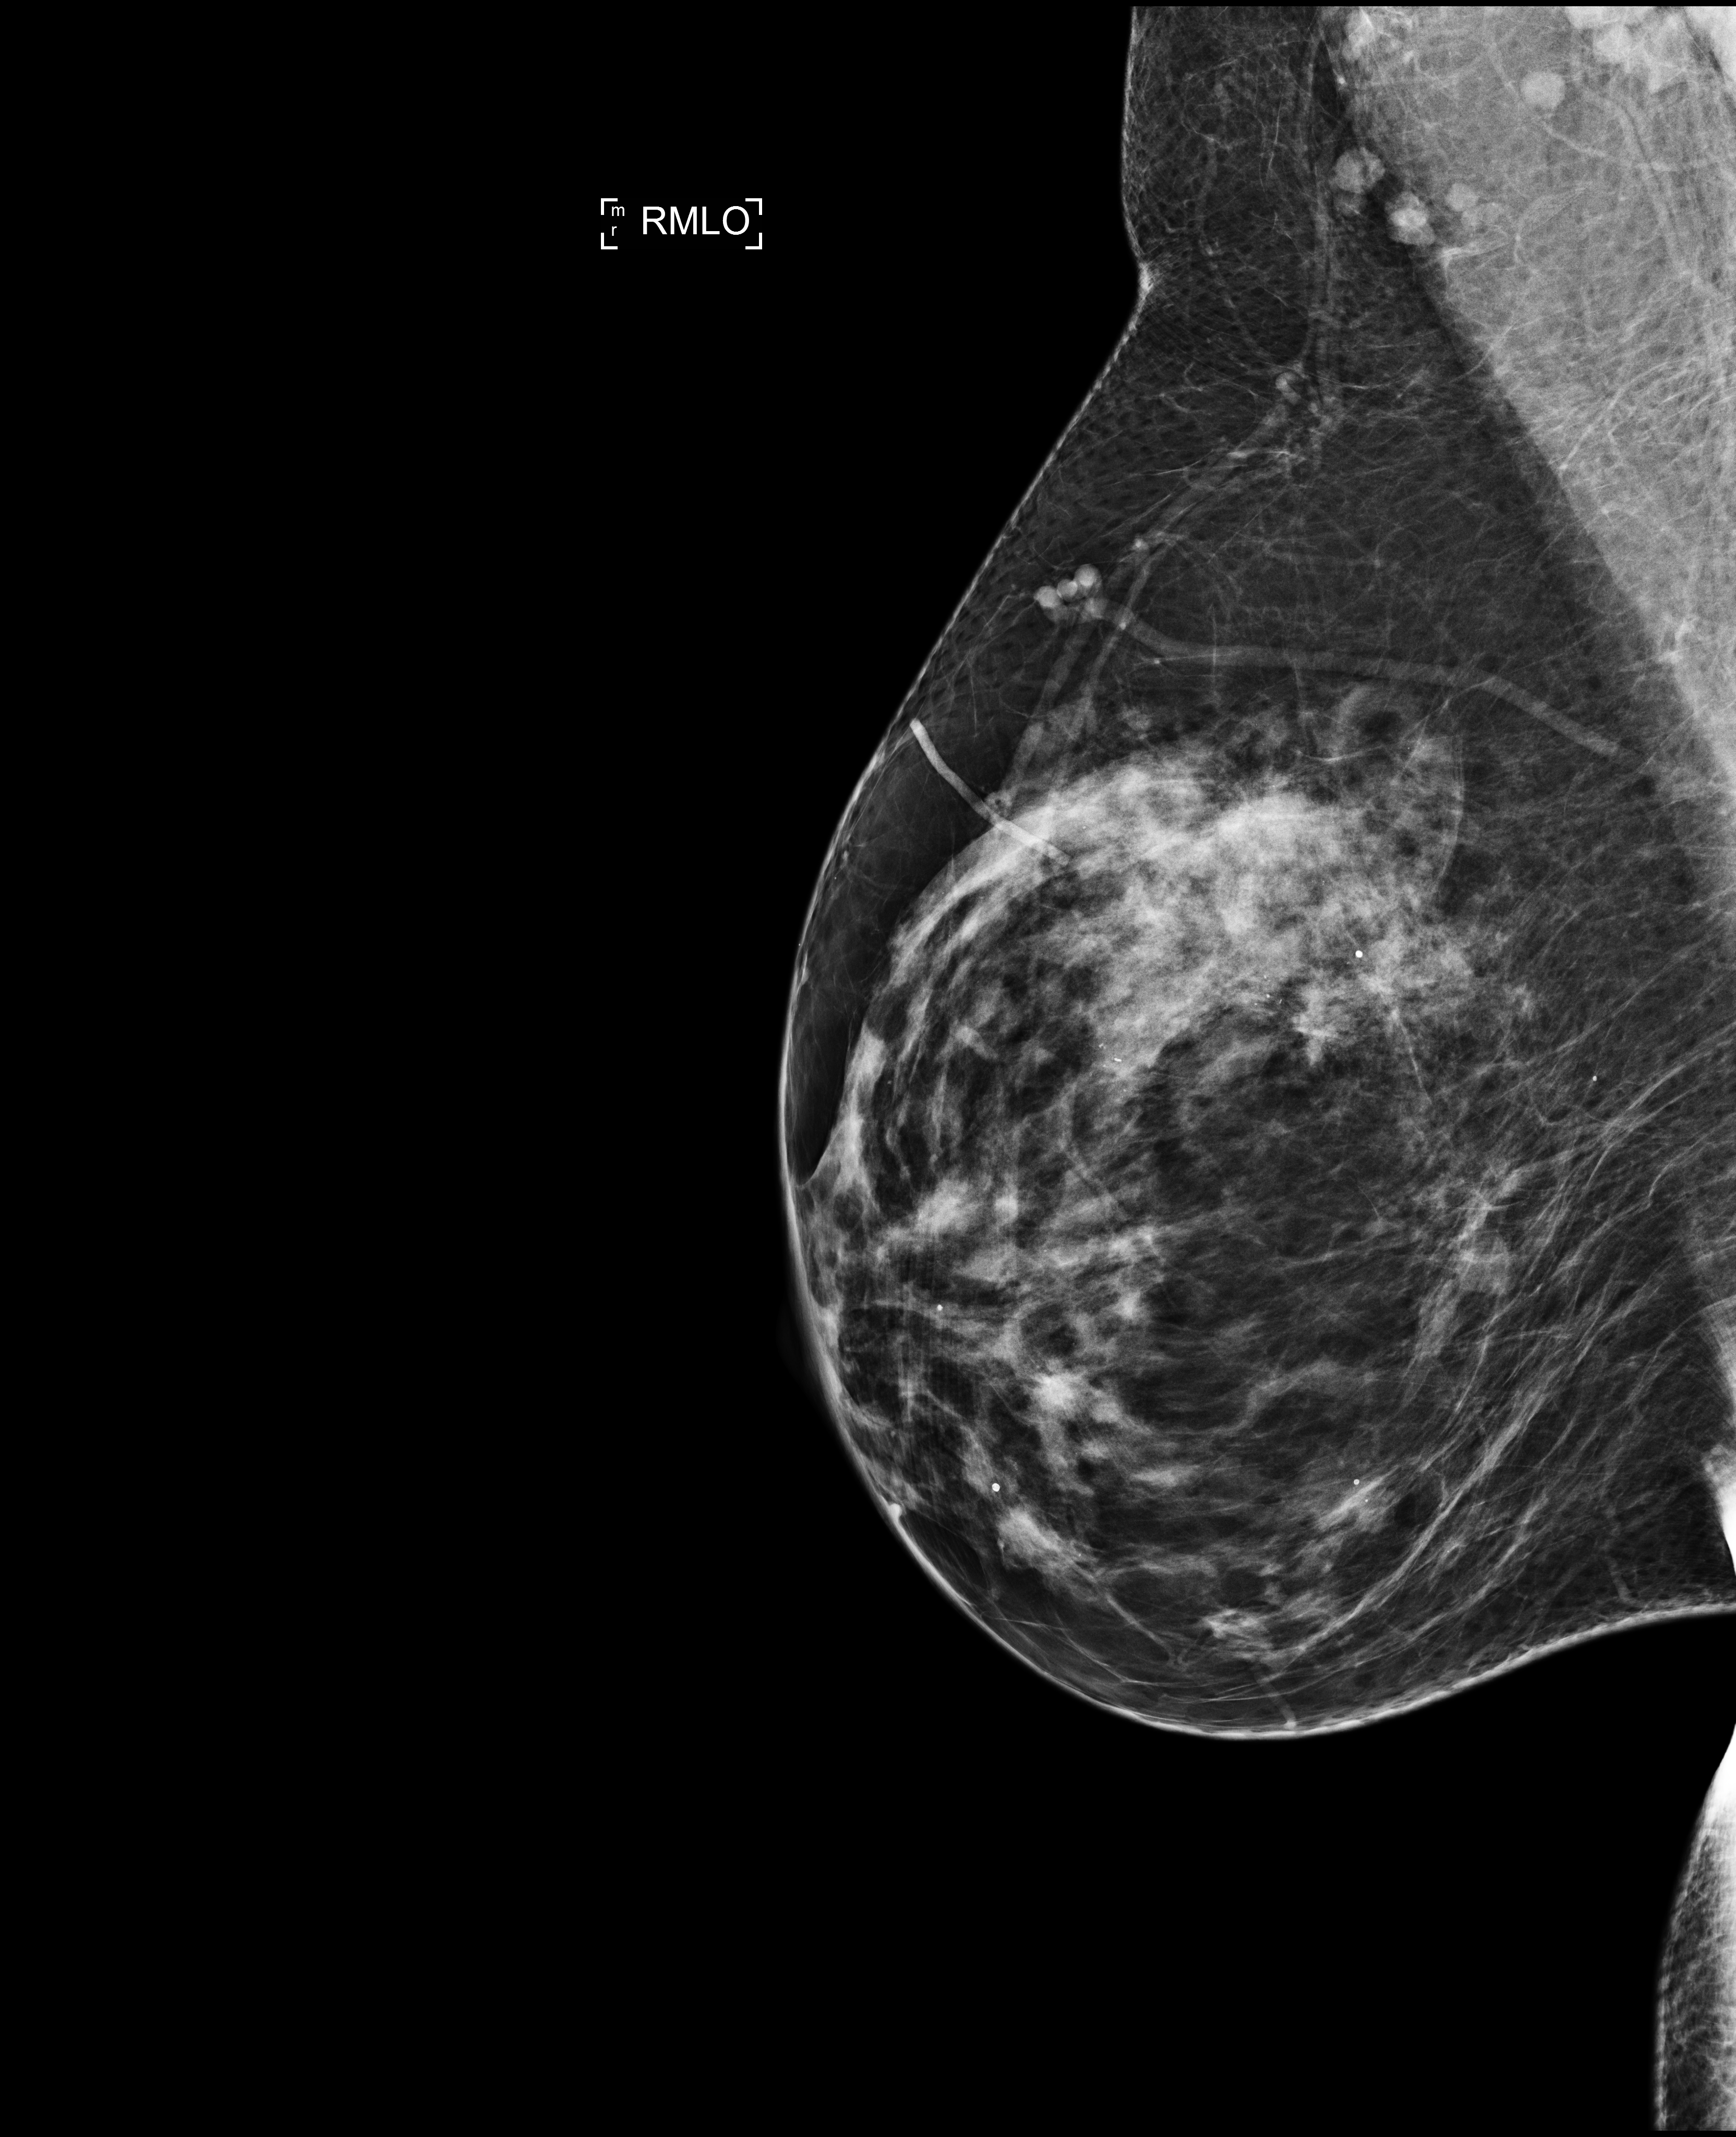
Annual screening mammography examination. Patient: female, 60 years.
Image type: full-field digital mammogram. Breast: right. Projection: medio-lateral oblique projection.